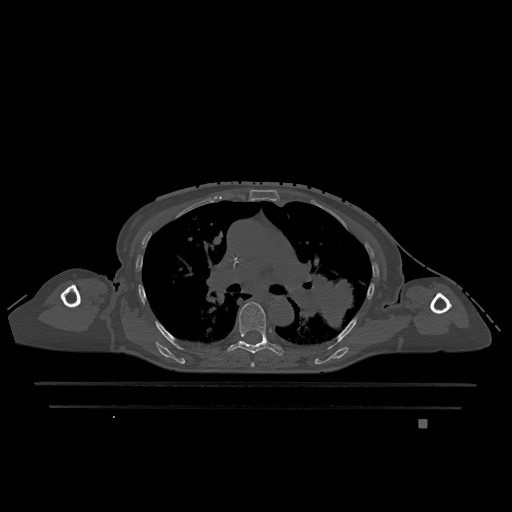
CT including the spine, one axial slice. Position 791 of 1317 along the scan axis. Bone window (W 1800 / L 400 HU). 0.5 mm slice thickness. 512 × 512 image matrix, field of view 500 × 500 mm. Patient: female, 74 years. From the clinical record (not read from this slice): primary cancer: lung; vertebrae with lytic lesions (as recorded): T1, T4, T5, T6, L4, L5.
Structures marked on this image (semi-automatic segmentation, software-assisted and operator-edited):
- T5 vertebra: bounding box (x1, y1, x2, y2) in pixels: (250, 362, 255, 367)
- T6 vertebra: (227, 302, 284, 356)